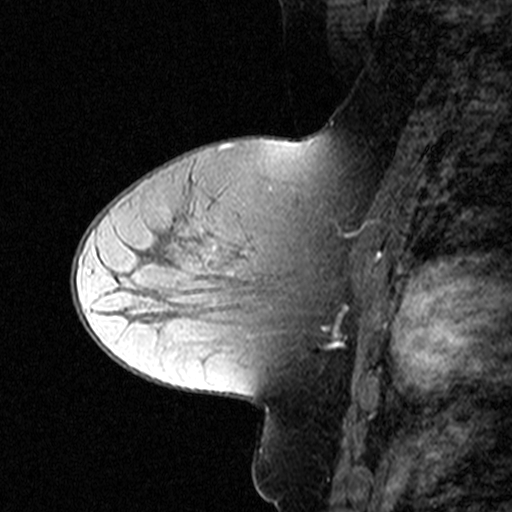
Breast MRI (dynamic contrast-enhanced), one sagittal slice. Position 25 of 44 along the scan axis. Dynamic contrast-enhanced study with each time point stored as its own series, time point 2 of 3 at this slice position (early post-contrast, ordered by acquisition time). 1.5 T. TE 4.5 ms, TR 11 ms. 3 mm slice thickness. 512 × 512 image matrix, field of view 200 × 200 mm. Patient: female, 50 years. Case-level facts recorded for this patient, not image findings: setting: breast cancer imaged before/during neoadjuvant chemotherapy; receptor status: HR-positive, HER2-negative.
Structures marked on this image (semi-automatically segmented with operator editing):
- analysis volume of interest (the breast-tissue region the enhancement analysis was run in; not a lesion): box from (x=180, y=198) to (x=349, y=311) px
- tumour enhancement mask (voxels above the 90 % enhancement threshold inside the analysis volume of interest): (x=343, y=306)–(x=346, y=308)